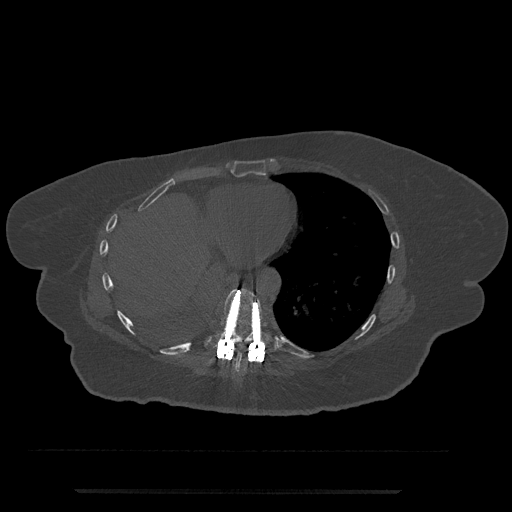
CT including the spine, one axial slice; position 350 of 797 along the scan axis; bone window (W 1800 / L 400 HU); 0.5 mm slice thickness; 512 × 512 image matrix, field of view 440 × 440 mm. Female patient, age 51 years. From the clinical record (not read from this slice): primary cancer: neuro.
Structures marked on this image (semi-automatically segmented with operator editing):
- T8 vertebra: bounding box (x1, y1, x2, y2) in pixels: (232, 344, 250, 373)
- T9 vertebra: (205, 288, 277, 362)